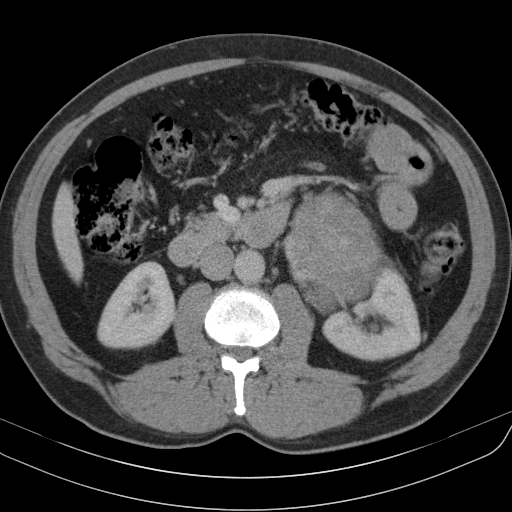
Contrast-enhanced abdominal CT, one axial slice. Position 56 of 91 along the scan axis. 130 kVp. Intravenous contrast given. Soft-tissue window (W 400 / L 40 HU). 512 × 512 image matrix, field of view 370 × 370 mm. Patient: male, 51 years. From the clinical record (not read from this slice): diagnosis: adrenocortical carcinoma; tumour side: left adrenal; tumour size at pathology: 18 cm; Ki-67 index: 40 %; stage (as recorded): 3.
Annotated regions visible in this slice (semi-automatic segmentation, software-assisted and operator-edited):
- mass: bounding box (x1, y1, x2, y2) in pixels: (286, 193, 391, 312)